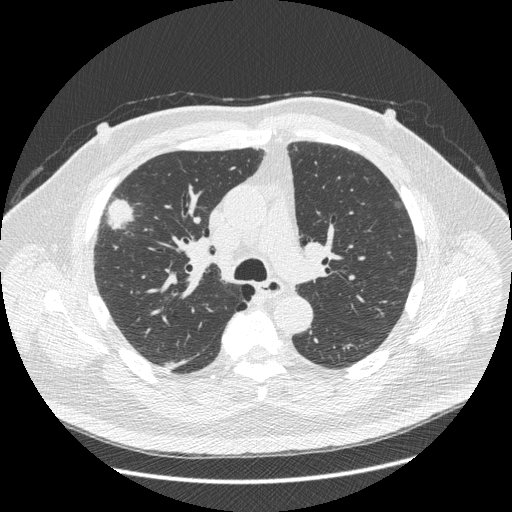
Low-dose screening chest CT, axial slice; third annual screen; lung window (W 1500 / L -600 HU); 512 × 512 image matrix. Male participant, aged 66 years at enrolment. Current smoker at enrolment.
Lesion marked by an expert reader, bounding box <86,181,145,264> (left, top, right, bottom; pixels). The exam's reader record, not a measurement of the box and not confirmed to be the same lesion: non-calcified nodule or mass ≥4 mm, right upper lobe, 48 × 25 mm, spiculated (stellate) margins, soft tissue attenuation, pre-existing on the prior screen: no. Lung cancer was diagnosed 35 days after this screen: non-small cell carcinoma, right upper lobe, stage IV (AJCC 6th edition), 50 mm at pathology.